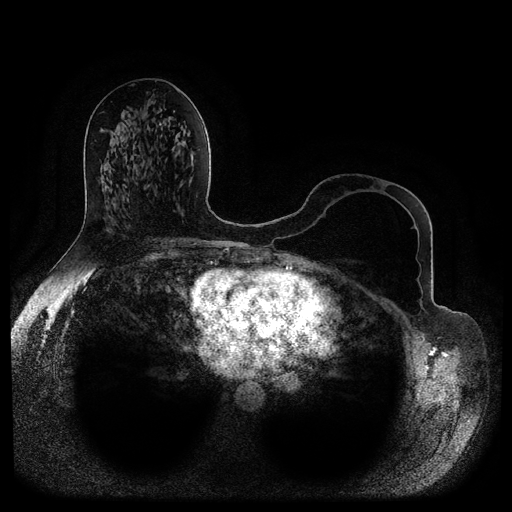
Breast MRI (dynamic contrast-enhanced, multi-phase), one axial slice; slice 48 of 116 in the series (ordered by position); dynamic contrast-enhanced series, time point 2 of 5 at this slice position (early post-contrast); 1.5 T; TE 2.6 ms, TR 5.2 ms; 512 × 512 image matrix, field of view 380 × 380 mm. Patient: female, 56 years.
Outlined on this slice (semi-automatic segmentation, software-assisted and operator-edited):
- breast lesion (labelled benign in the annotation): bounding box [x1, y1, x2, y2] px = [159, 122, 163, 145]